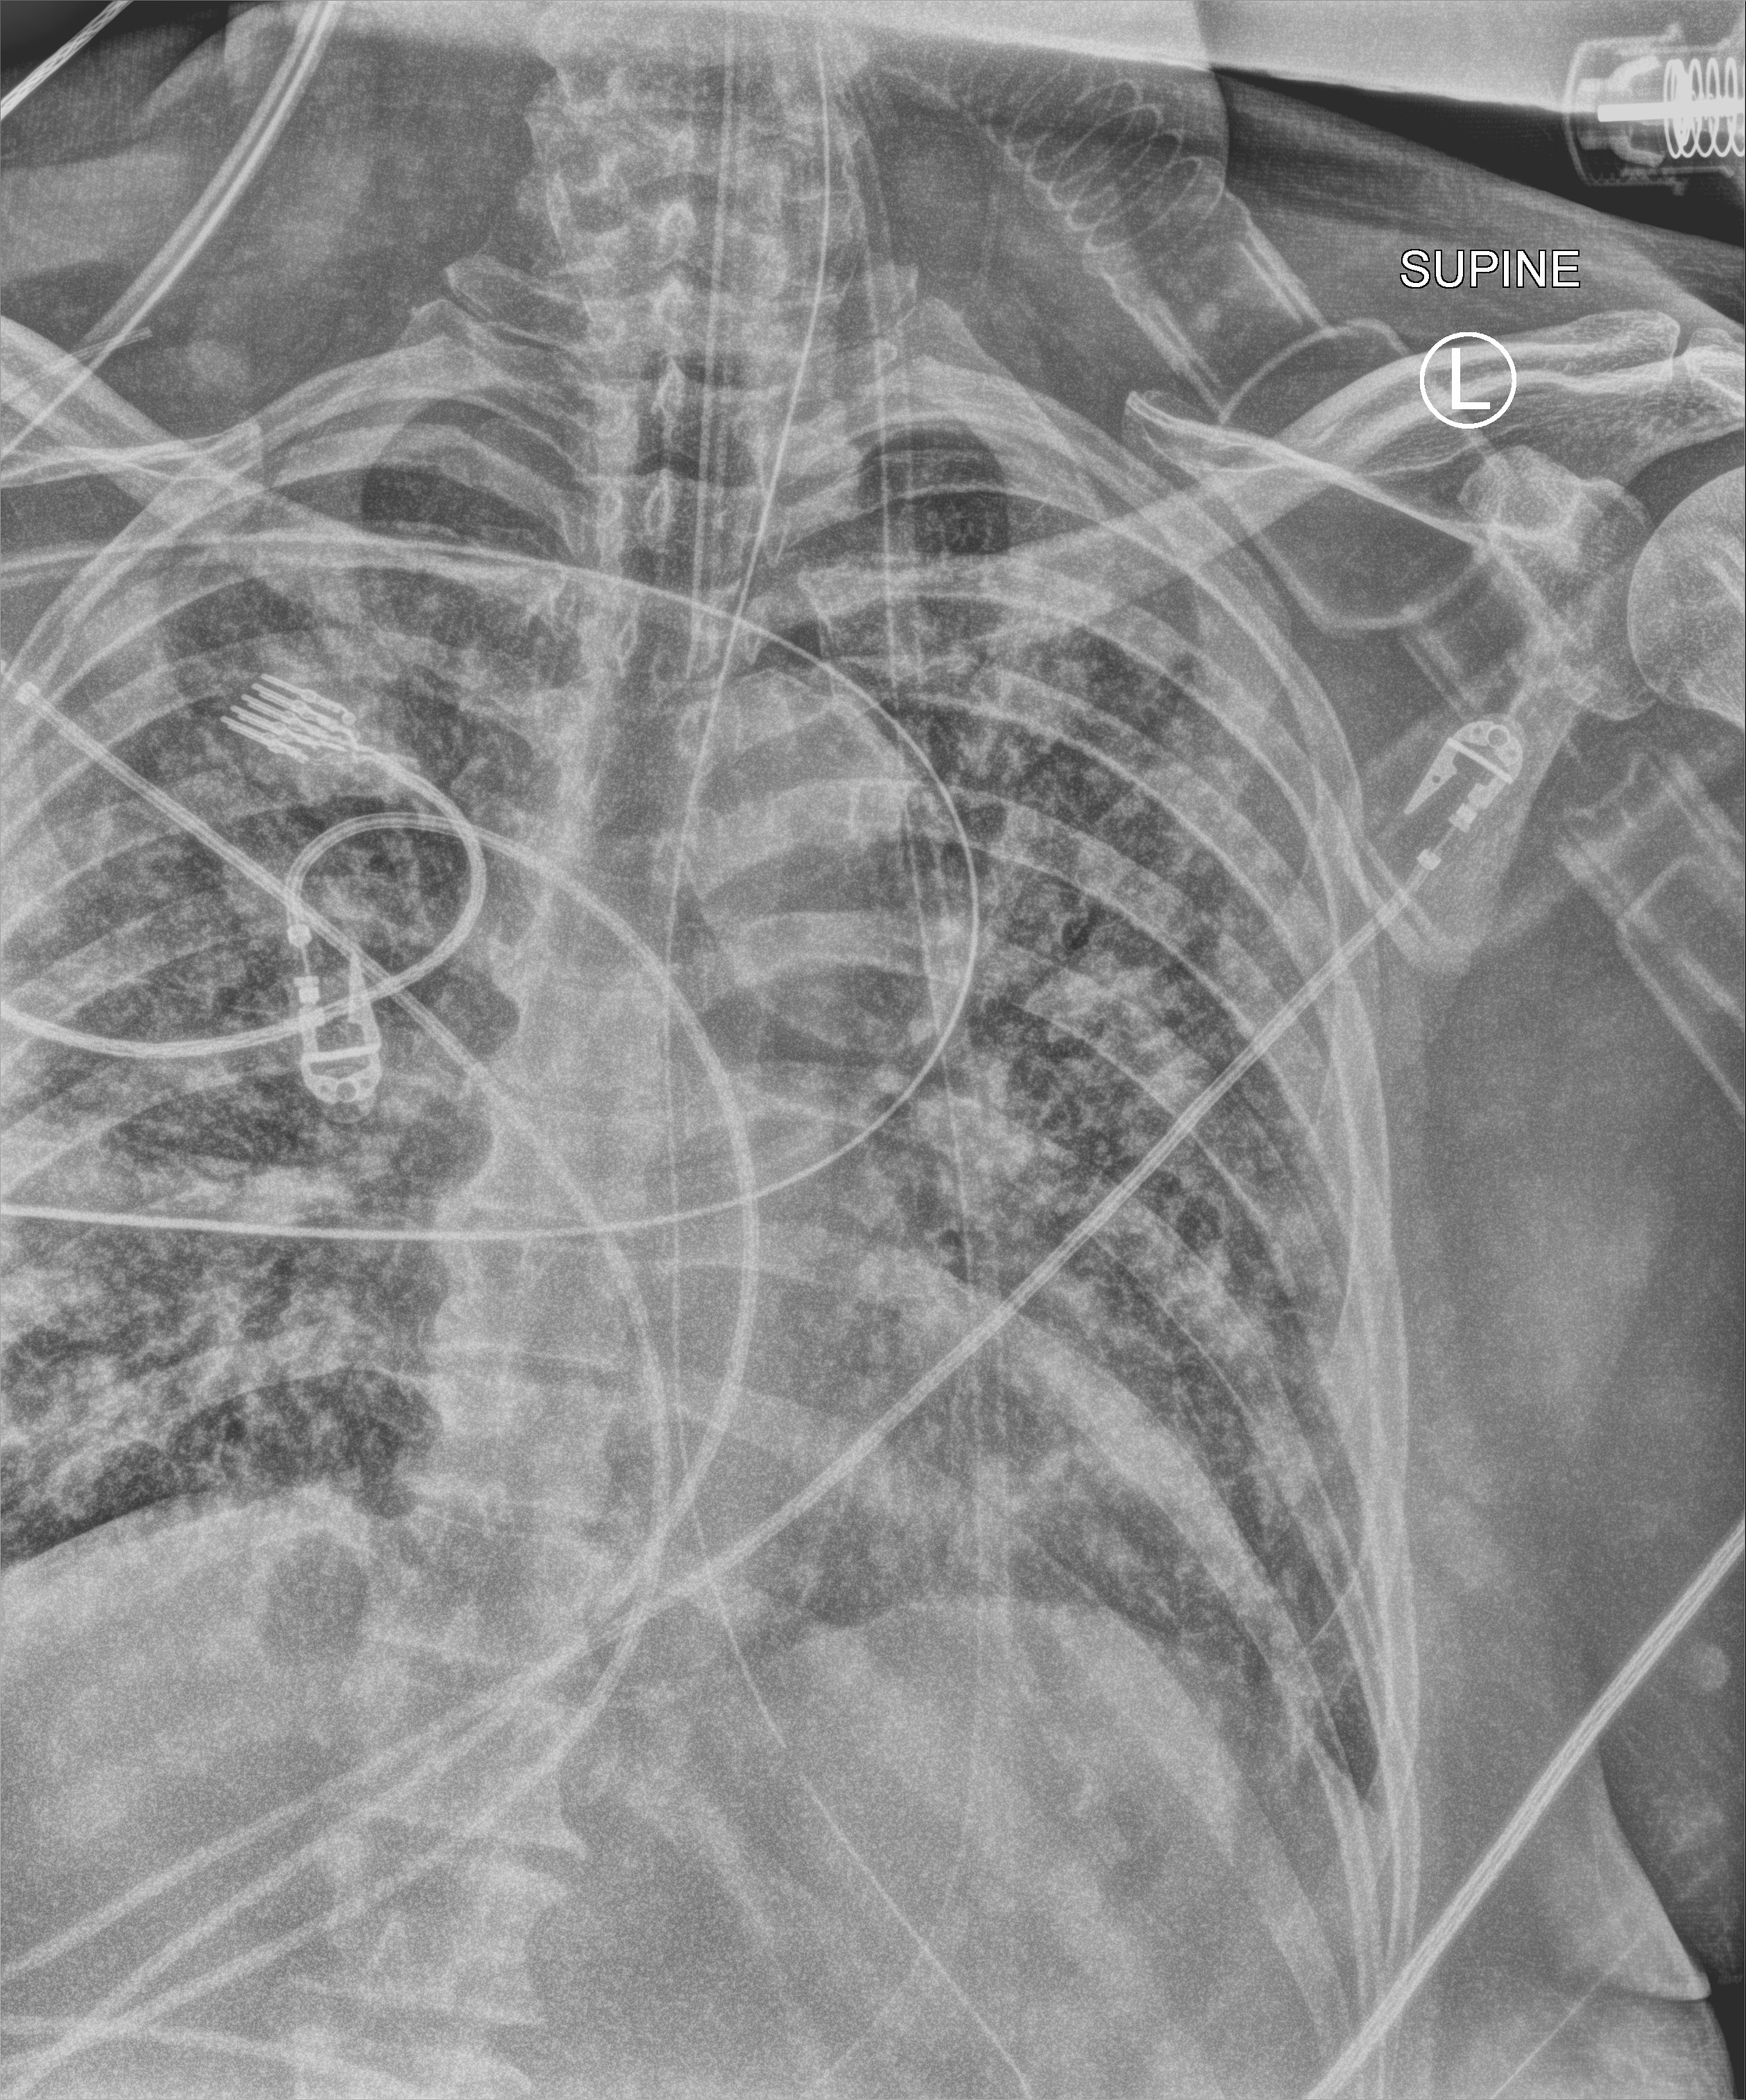
Portable chest radiograph, anteroposterior (AP) projection. Male patient hospitalised with COVID-19, age 60–74 years.
Admission-level facts for this patient (not findings on this image; timing relative to this image not recorded): mechanically ventilated during this hospital stay: yes.